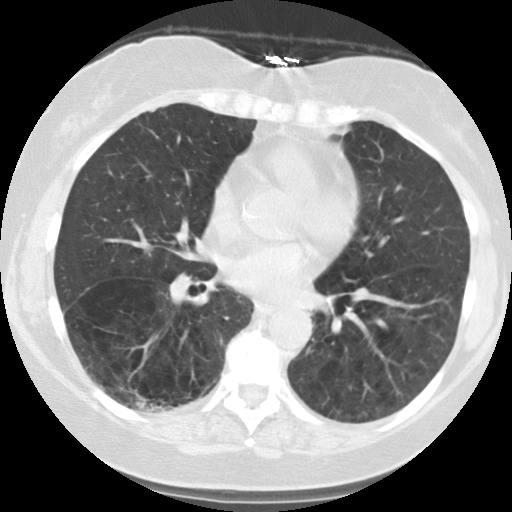
Low-dose screening chest CT, one axial slice; slice 54 of 122 in the series (ordered by position); reconstruction kernel STANDARD; lung window (W 1500 / L -600 HU); 512 × 512 image matrix.
Annotated regions visible in this slice (outlined manually by an expert reader):
- lesion 1 (tumor, lower lobe of right lung): bounding box (x1, y1, x2, y2) in pixels: (135, 396, 175, 410)